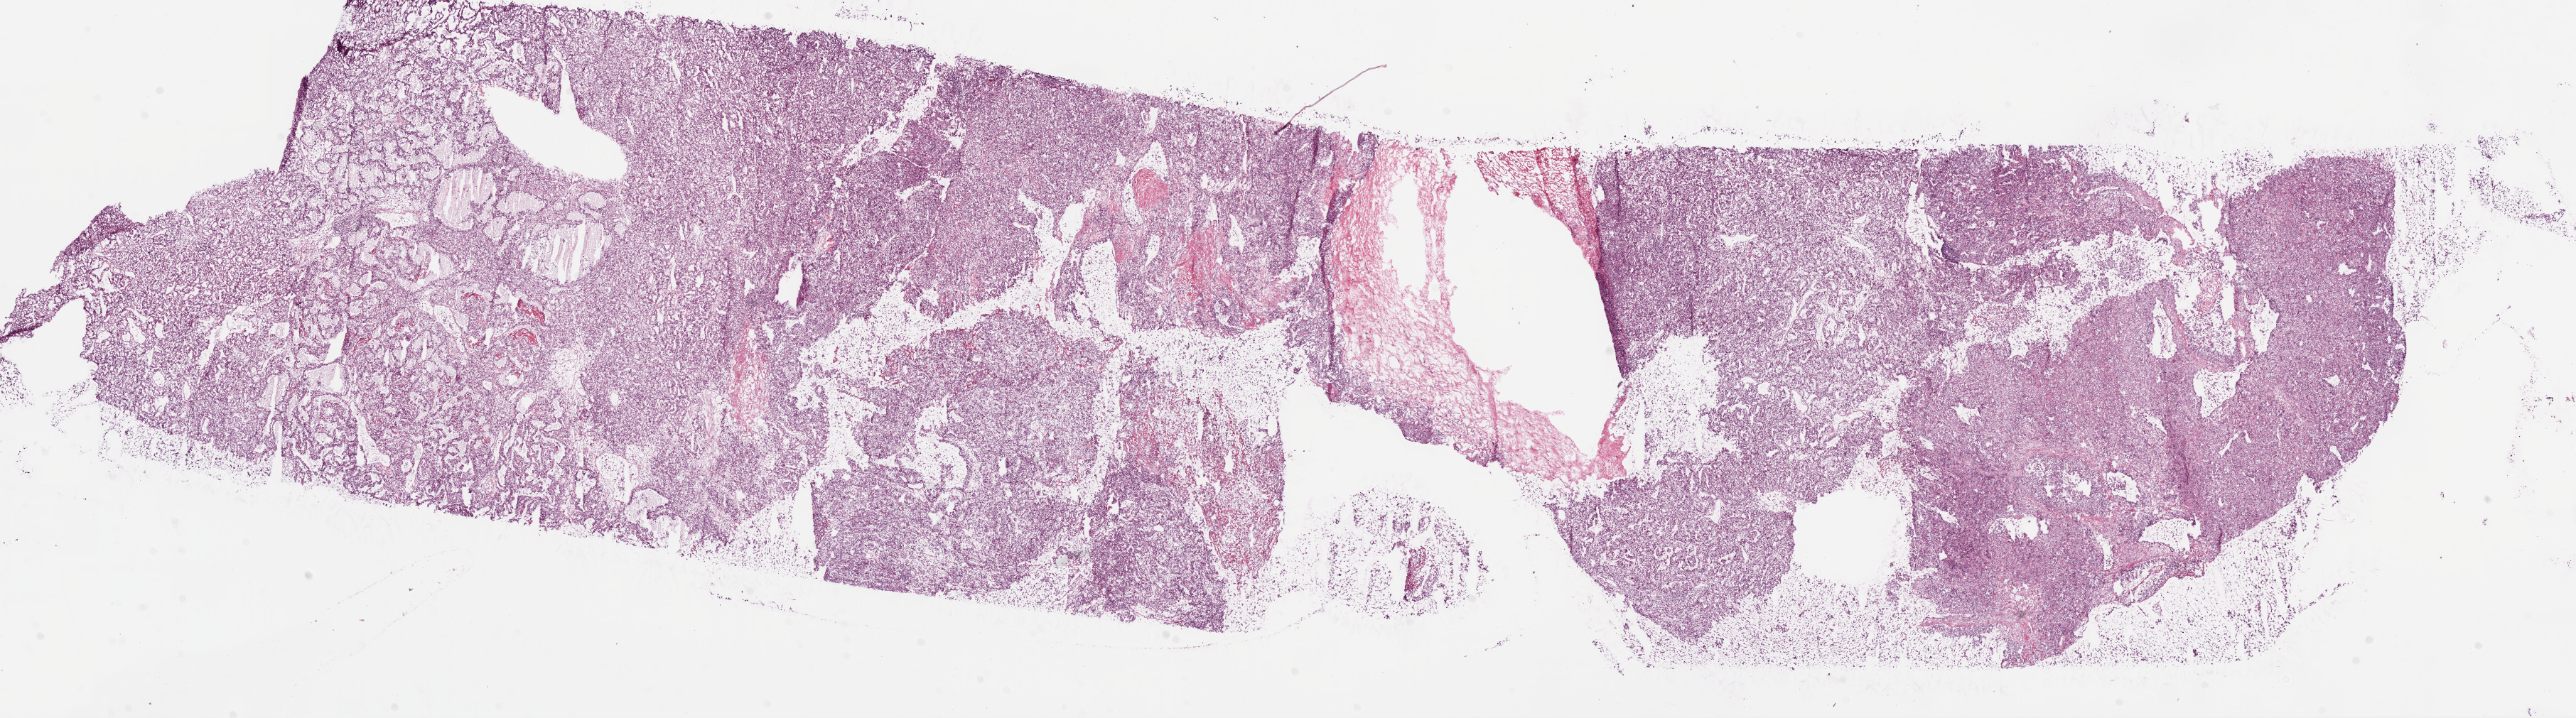
H&E whole-slide image, a low-resolution overview of the entire scanned area, about 29.1 x 8.1 mm; frozen section; sample: primary tumour, kidney. Patient: male, age at initial diagnosis 49 years. Histologic grade: G2 (moderately differentiated). Composition of this section per pathologist review: tumour cells 82%, tumour nuclei 80%, normal cells 0%, stromal cells 15%, necrosis 3%.
AJCC pathologic stage: III. Laterality: right. Histologic diagnosis: Clear cell adenocarcinoma, NOS.